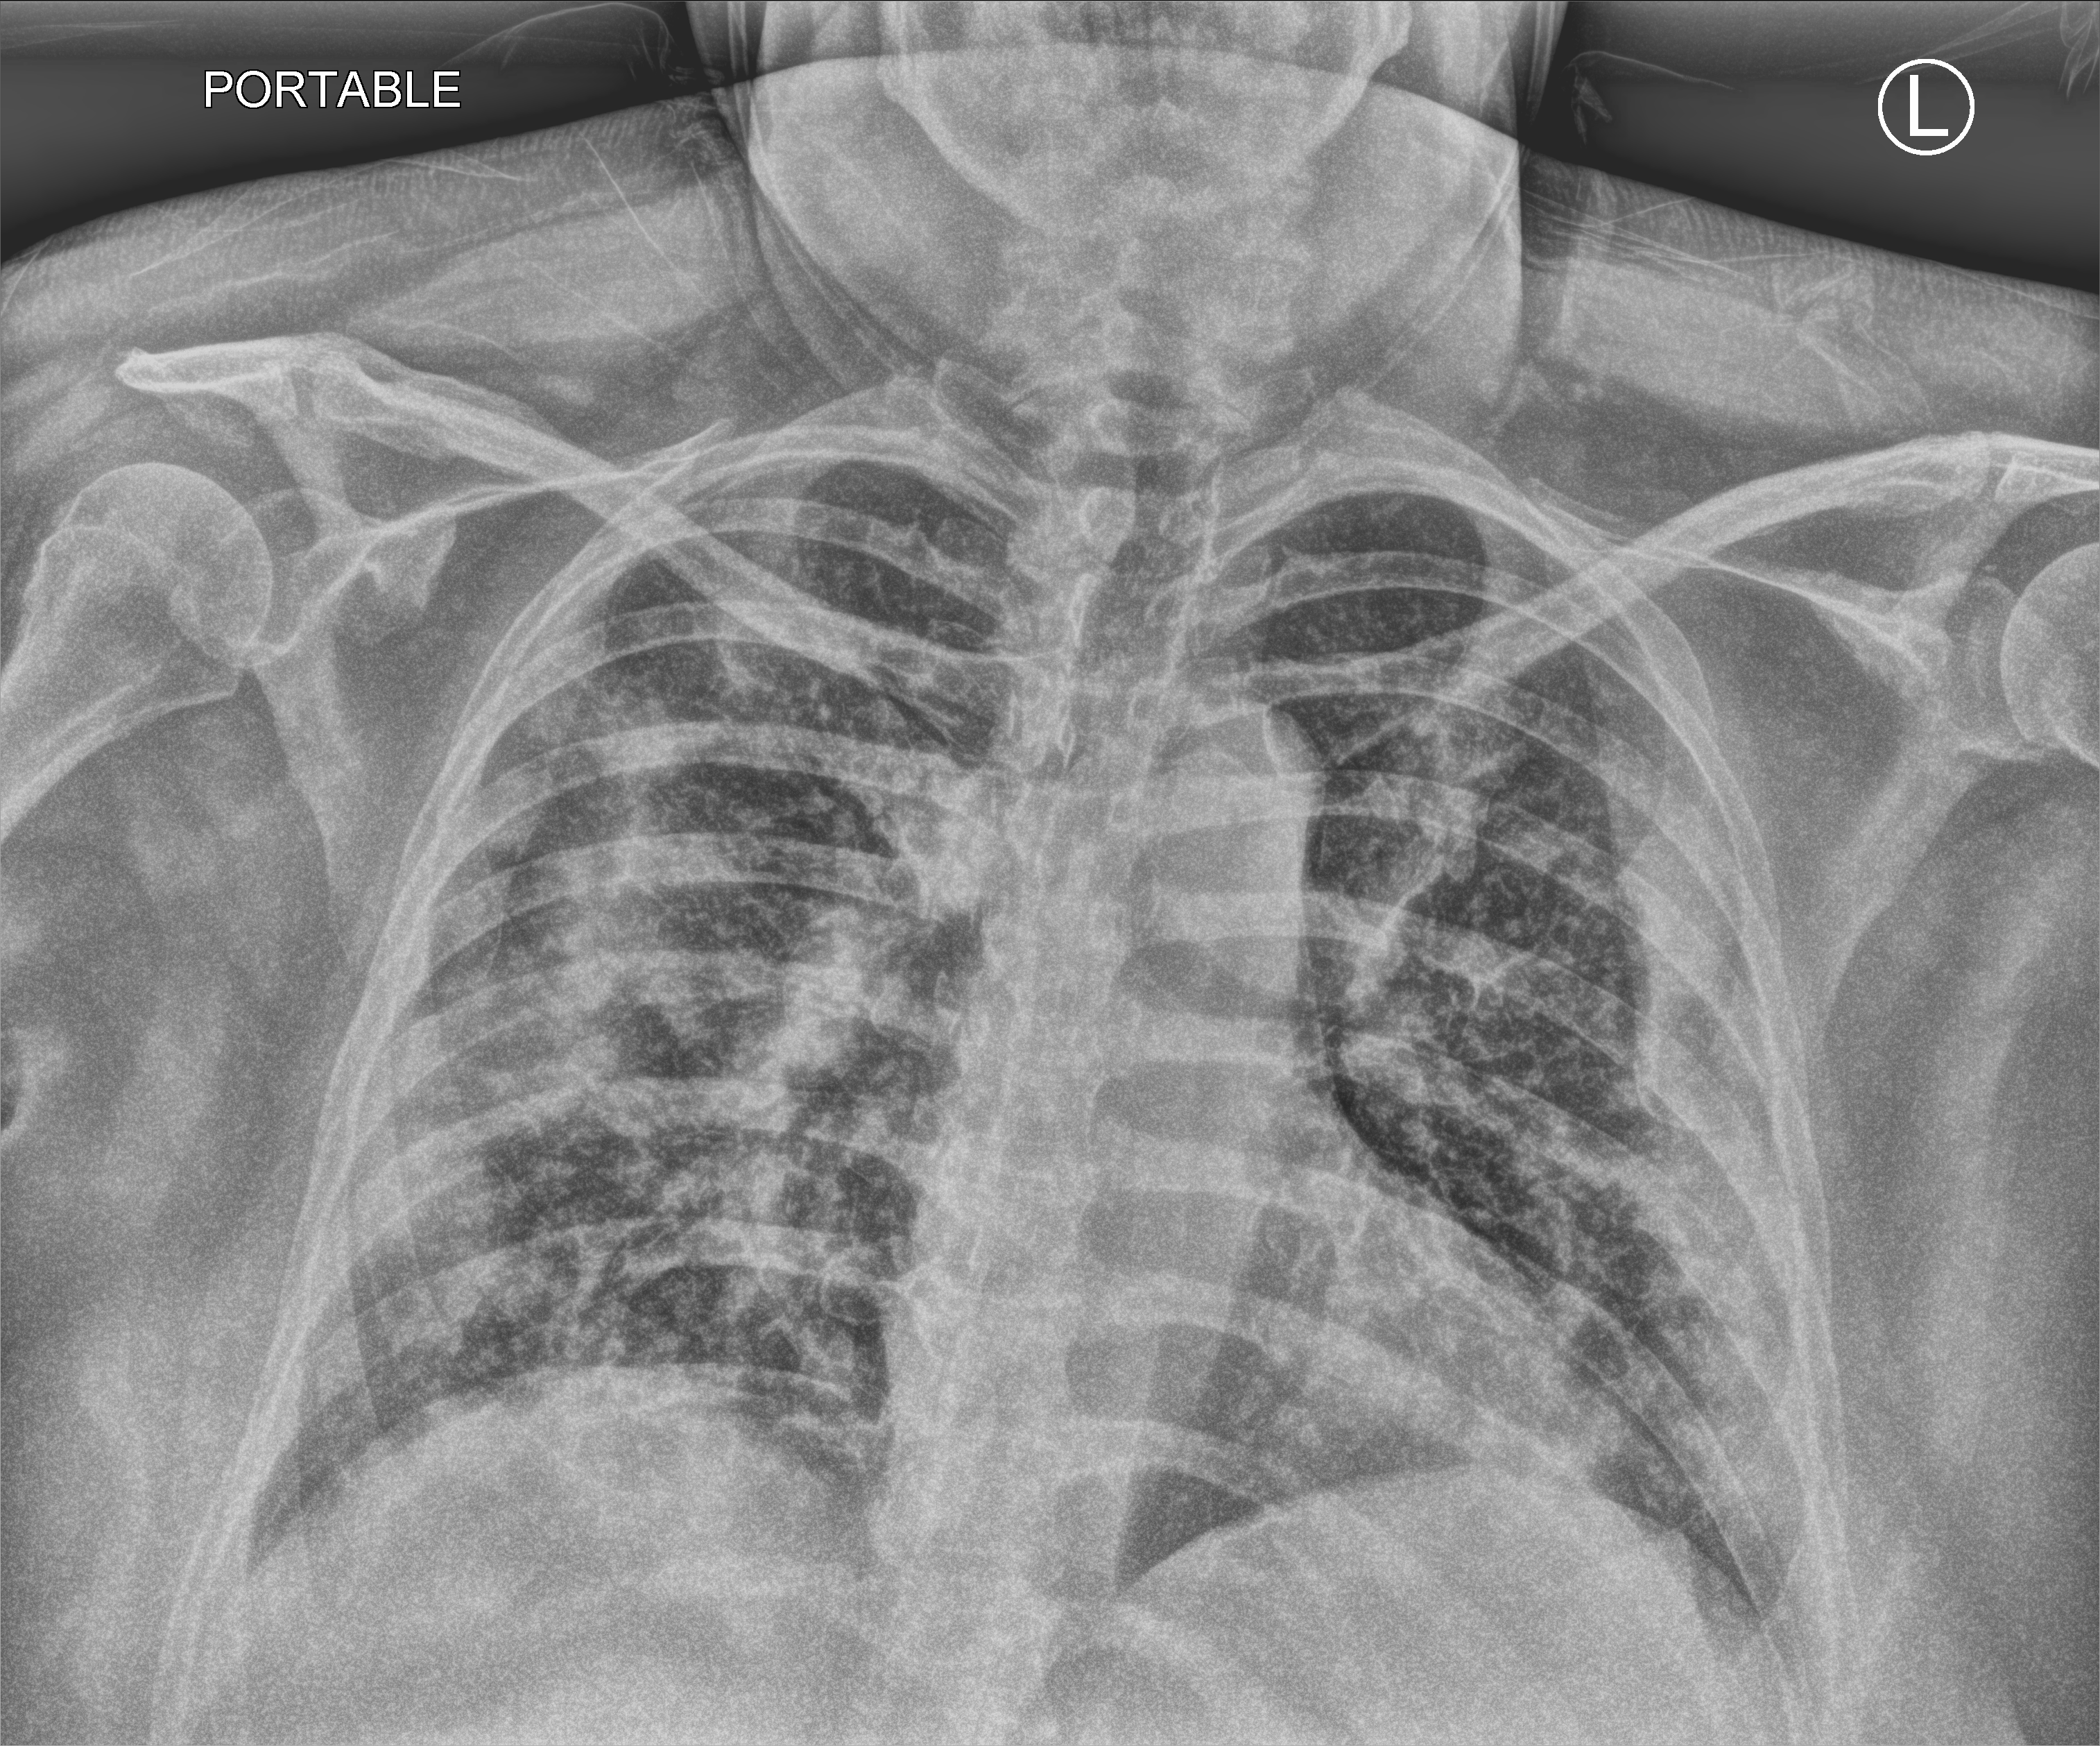
Chest X-ray (portable), anteroposterior (AP) projection. Patient hospitalised with COVID-19; female, aged 18–59 years.
Hospital-stay facts (about this admission, not read from this image; timing relative to this image not recorded):
- mechanically ventilated during this hospital stay: no
- admitted to intensive care during this hospital stay: no